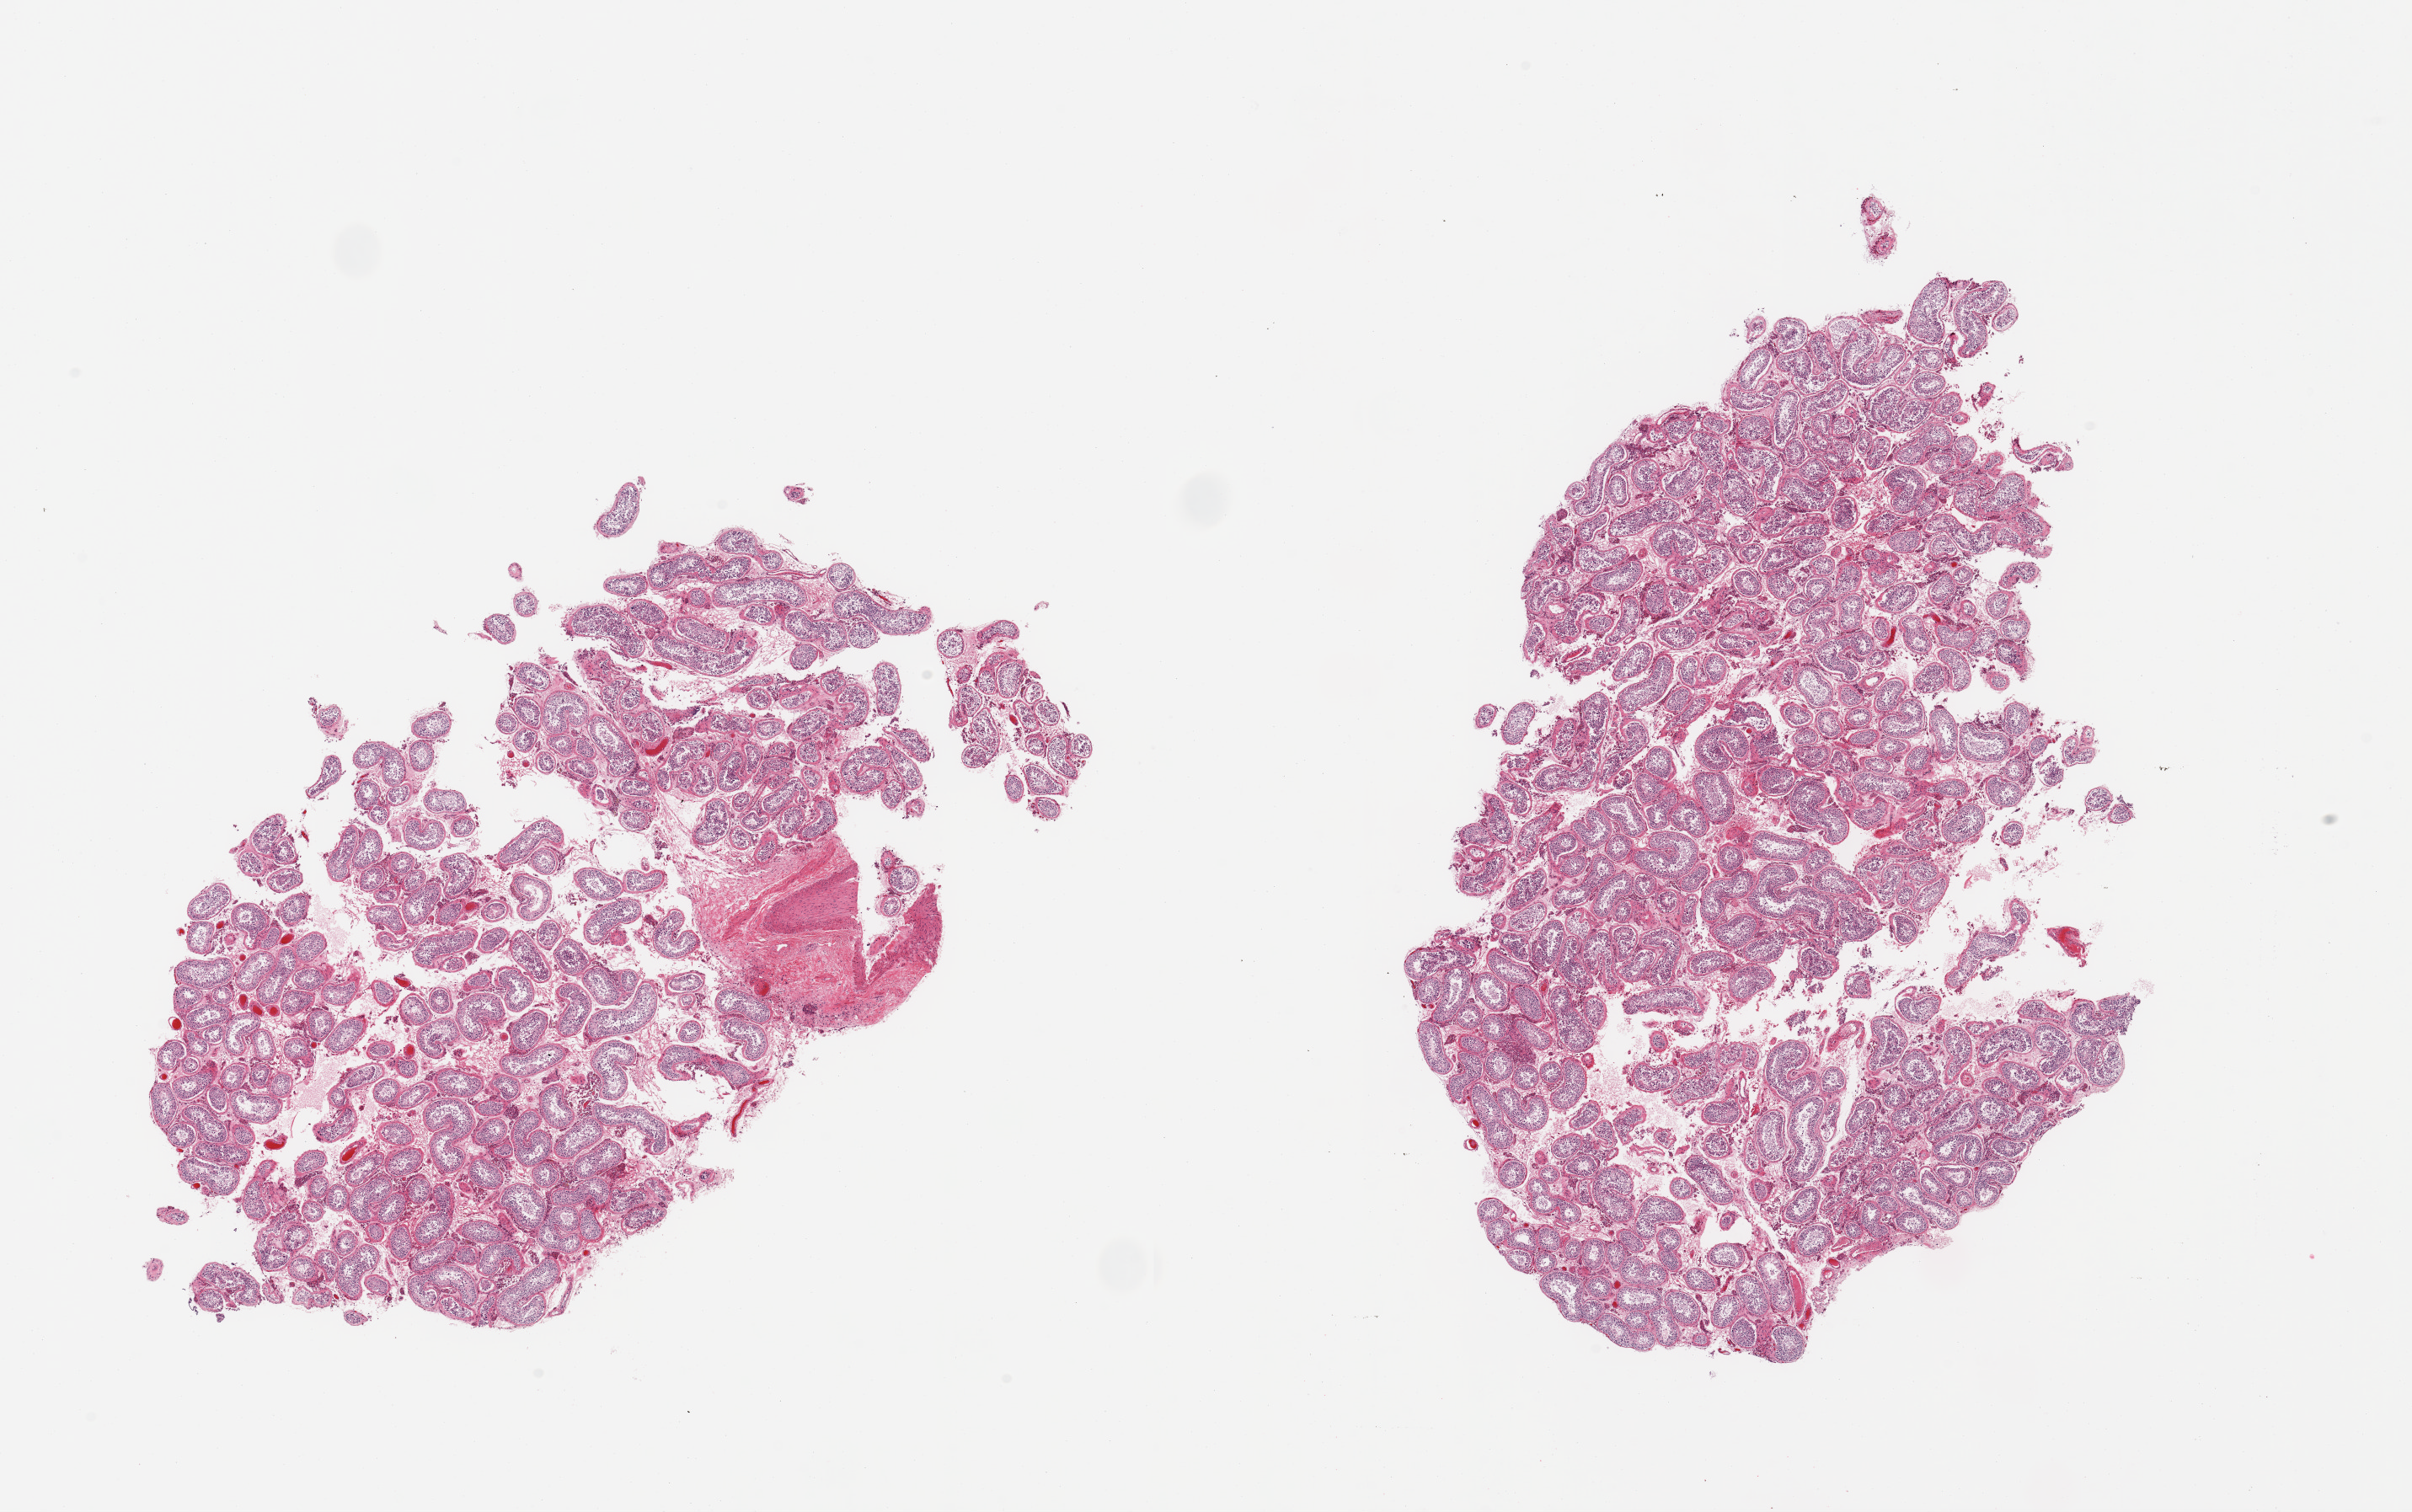
Hematoxylin and eosin (H&E) whole-slide image, a low-resolution overview of the entire scanned area, about 22.6 x 14.2 mm, PAXgene-fixed, paraffin-embedded tissue, target tissue: testis, donor tissue sample. Male donor.
Review note (as recorded): 2 pieces, focal areas are score 2. Spermatogenesis is present.